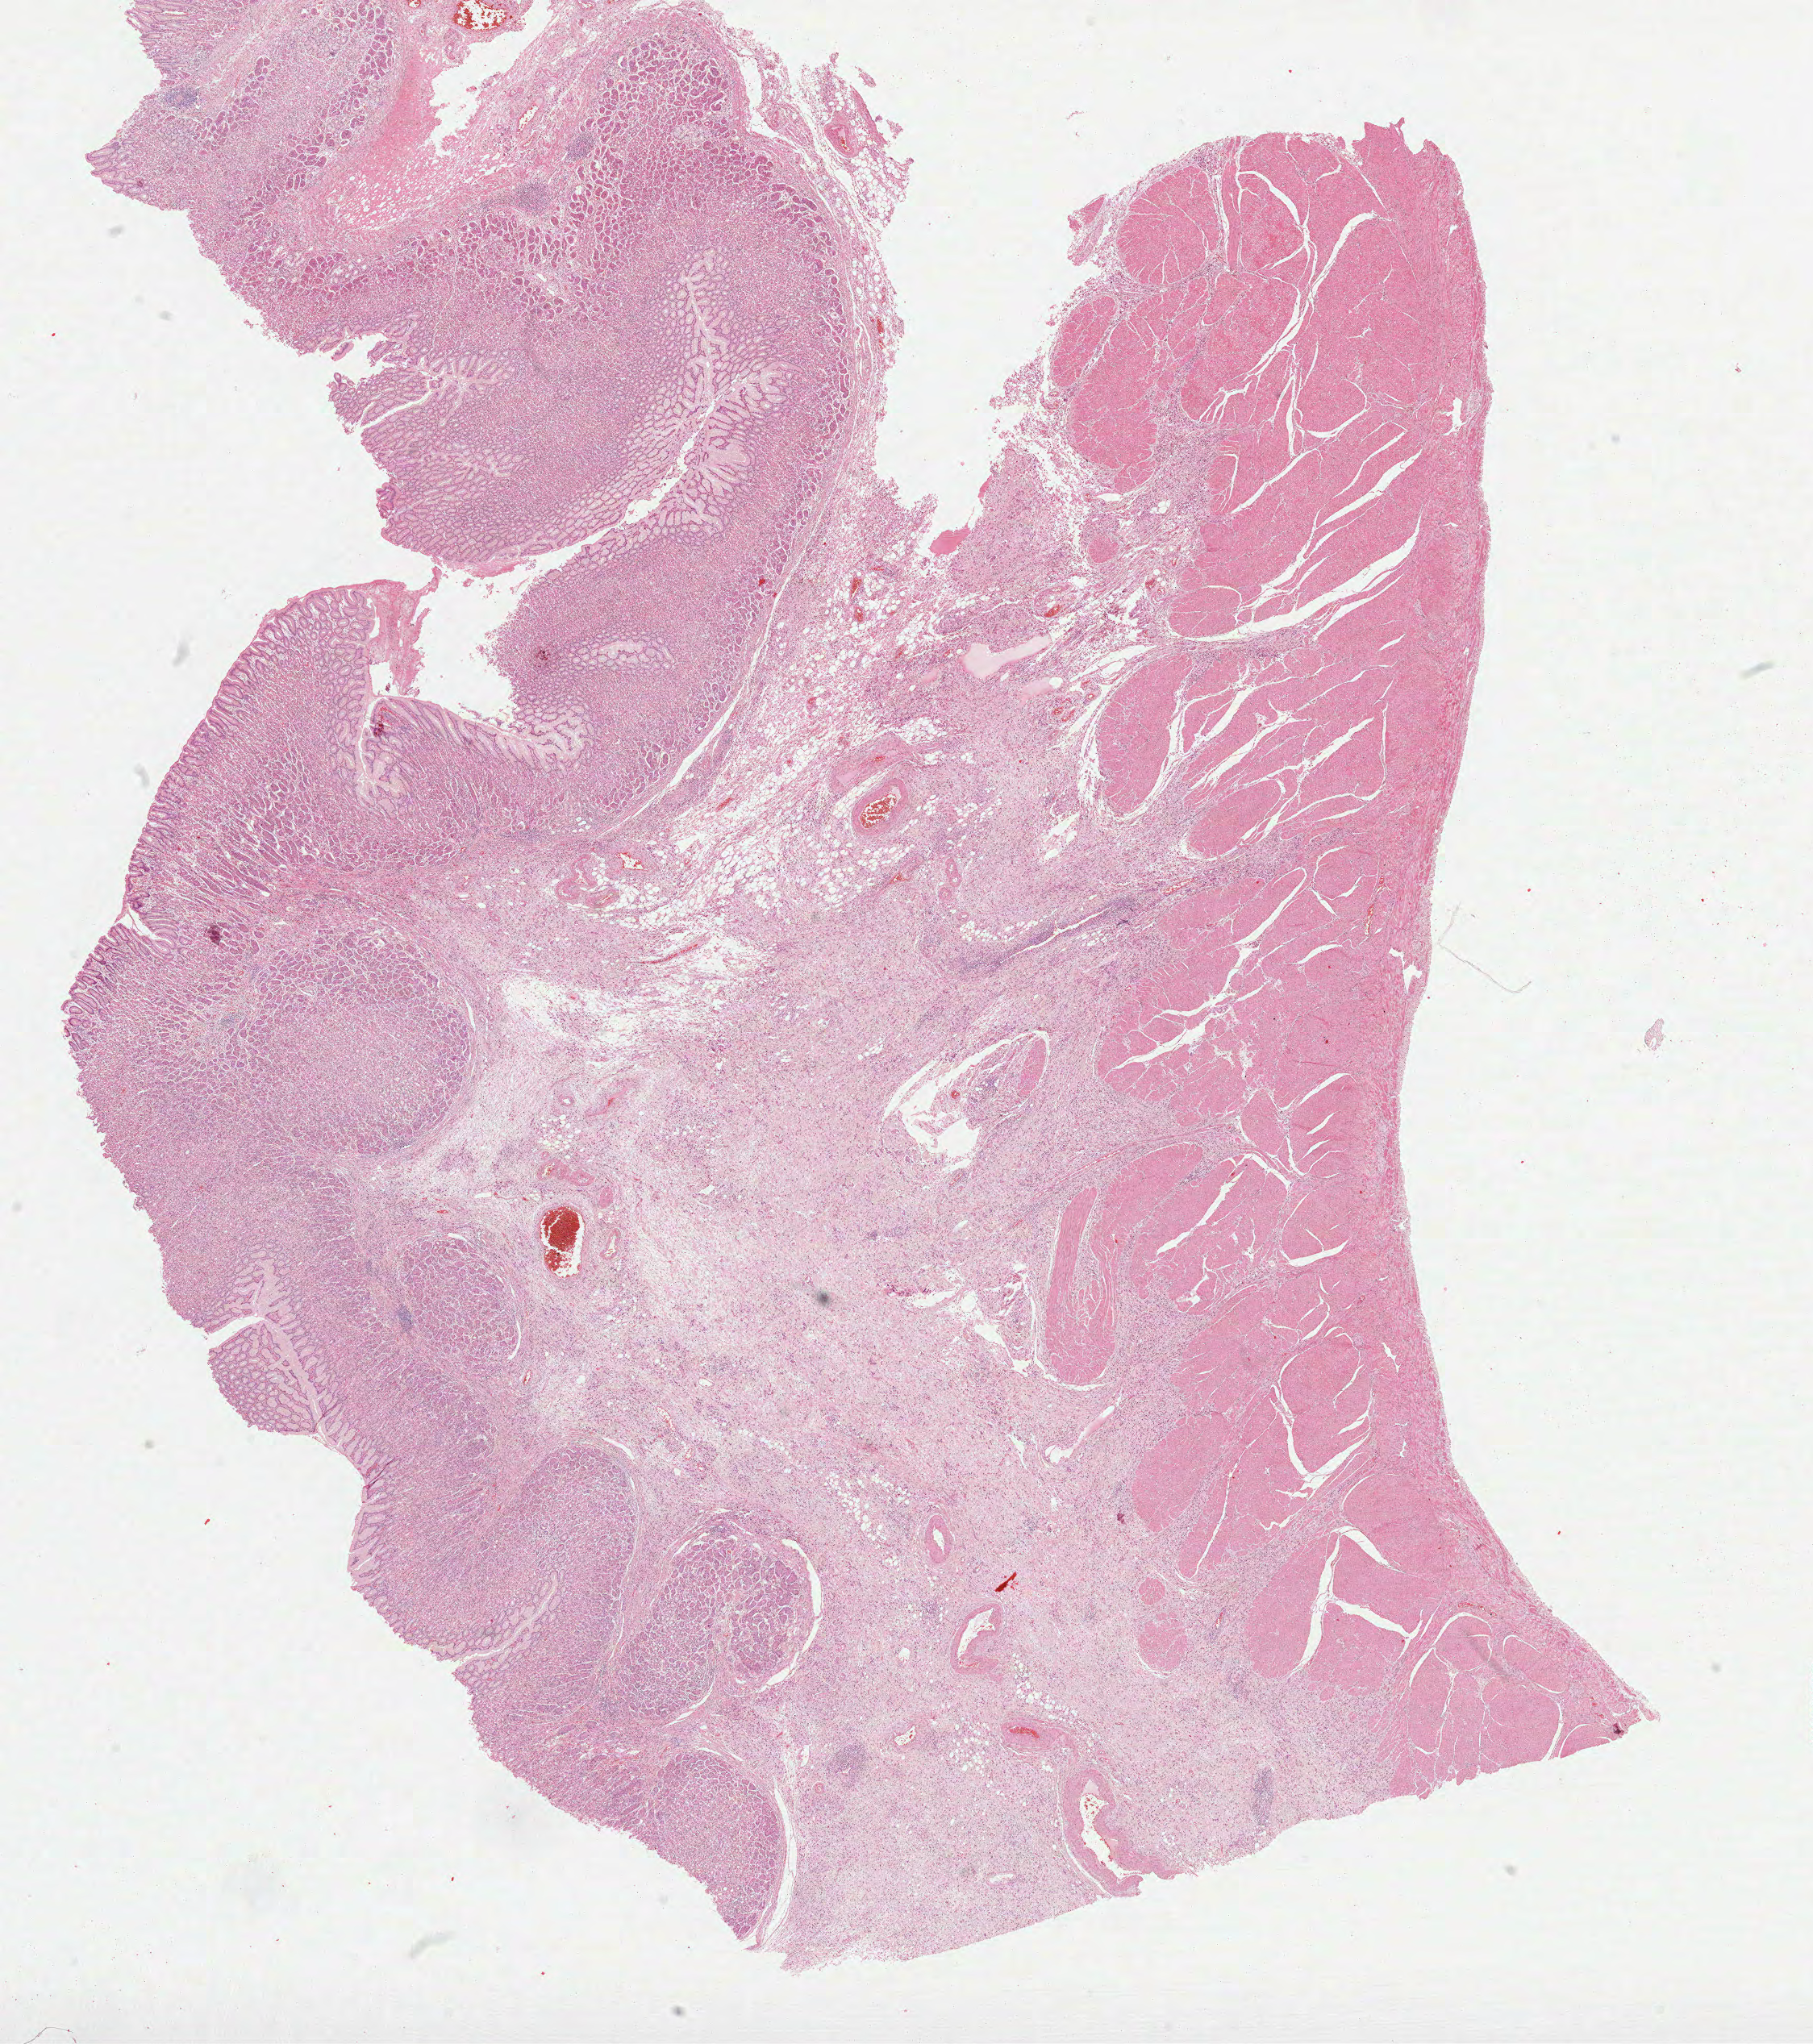
Digitized H&E-stained tissue section (whole slide) — low-resolution overview of the scanned area, about 18.1 x 20.4 mm (acquisition: 40x scan). Formalin-fixed paraffin-embedded (FFPE) diagnostic section. Sample: primary tumour, stomach. Male patient; age at initial diagnosis 75 years. Histologic grade: G3 (poorly differentiated).
AJCC pathologic stage: IIIA (7th edition). Pathologic diagnosis: Carcinoma, diffuse type (cardia, NOS). Lymph nodes positive (case pathology): 17 of 20 examined.